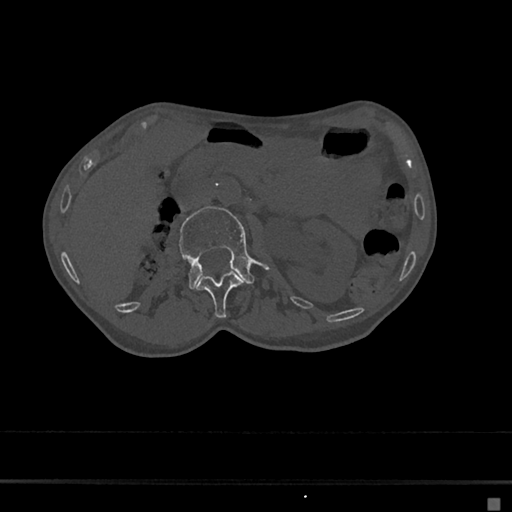
CT including the spine, one axial slice; slice 39 of 797 in the series (ordered by position); reconstruction kernel Br40s/3; bone window (W 1800 / L 400 HU); 0.5 mm slice thickness; 512 × 512 image matrix. Patient: female, 68 years. From the clinical record (not read from this slice): primary cancer: renal.
Structures marked on this image (semi-automatically segmented with operator editing):
- L1 vertebra: bounding box [x1, y1, x2, y2] px = [196, 271, 243, 319]
- L2 vertebra: [178, 206, 268, 288]